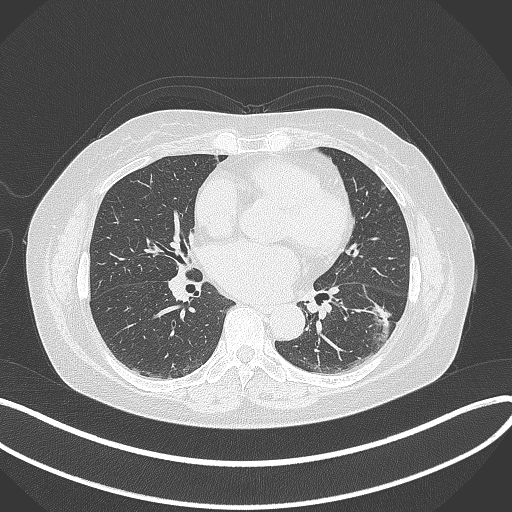
Chest CT, one axial slice; position 169 of 373 along the scan axis; reconstruction kernel B70f; 120 kVp; lung window (W 1500 / L -600 HU); 512 × 512 image matrix, field of view 400 × 400 mm. Female patient, age 67 years. From the clinical record (not read from this slice): clinical TNM (as recorded): T1c N0 M0; histopathological grade: G2.
Outlined on this slice (rectangle marked by the reading radiologist):
- lung tumour (recorded histology: adenocarcinoma): bounding box <360,299,394,351> (left, top, right, bottom; pixels)